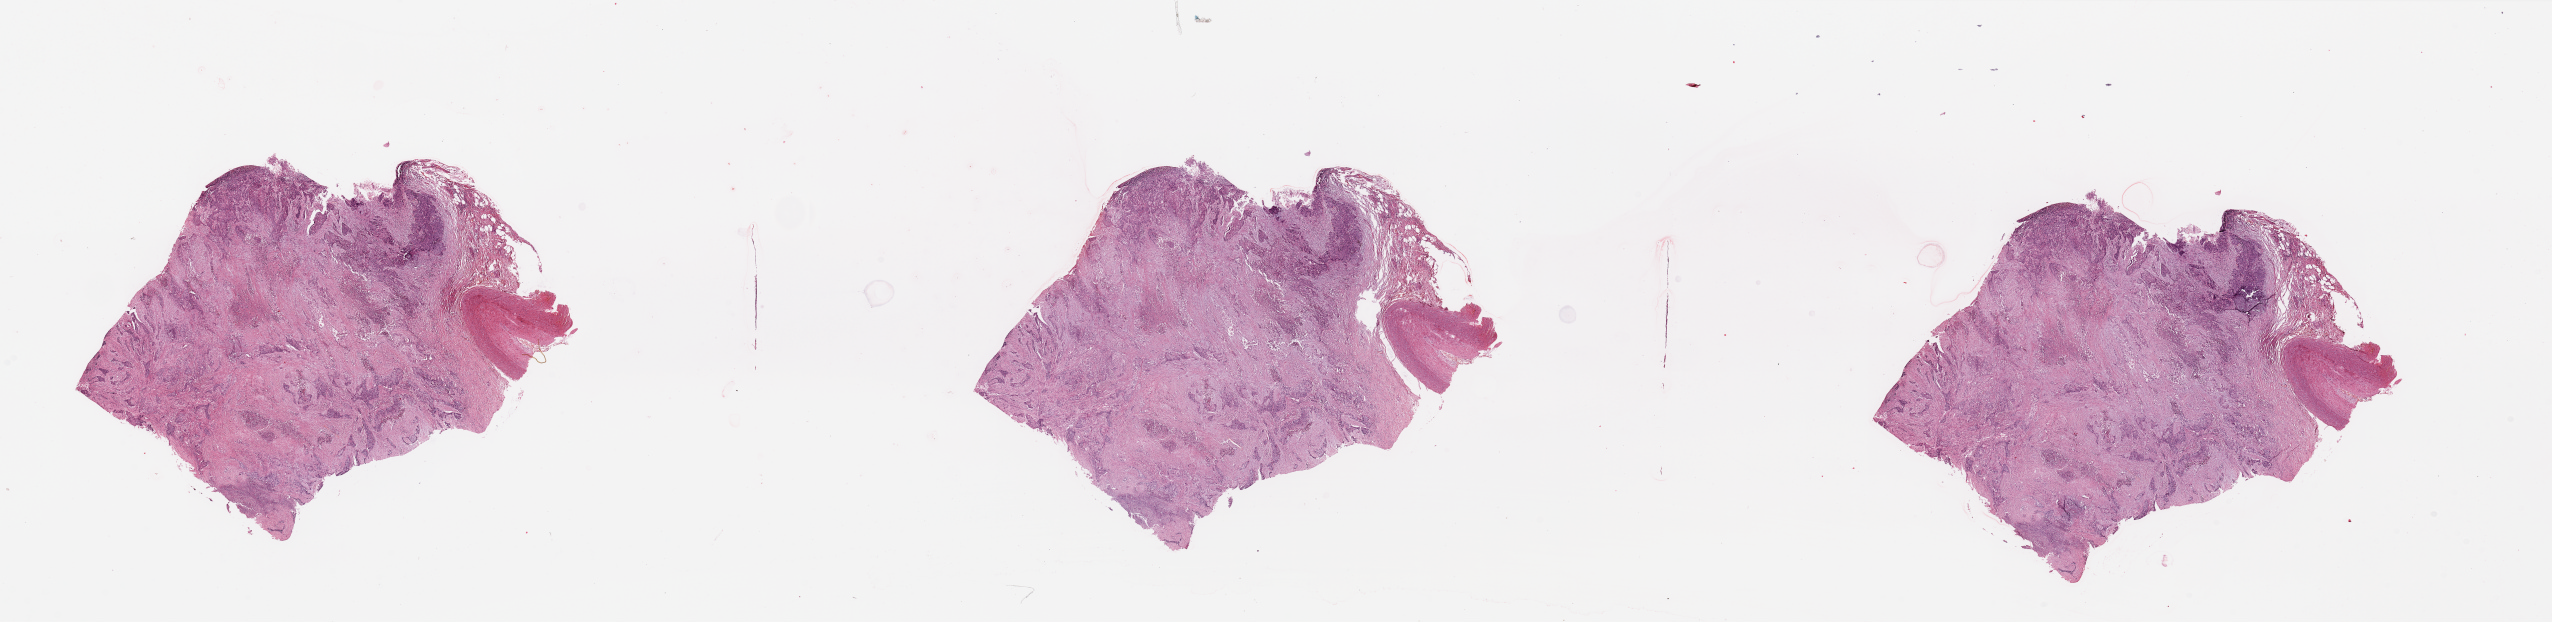
Whole-slide histology image, H&E-stained — low-resolution overview of the scanned area, about 40.4 x 9.8 mm. Lung, tumour tissue. Male, 73 y/o. Histologic grade: G2 (moderately differentiated).
AJCC pathologic stage: II. Primary tumour site (as recorded): right middle lobe. Diagnosis: Squamous cell carcinoma, NOS.